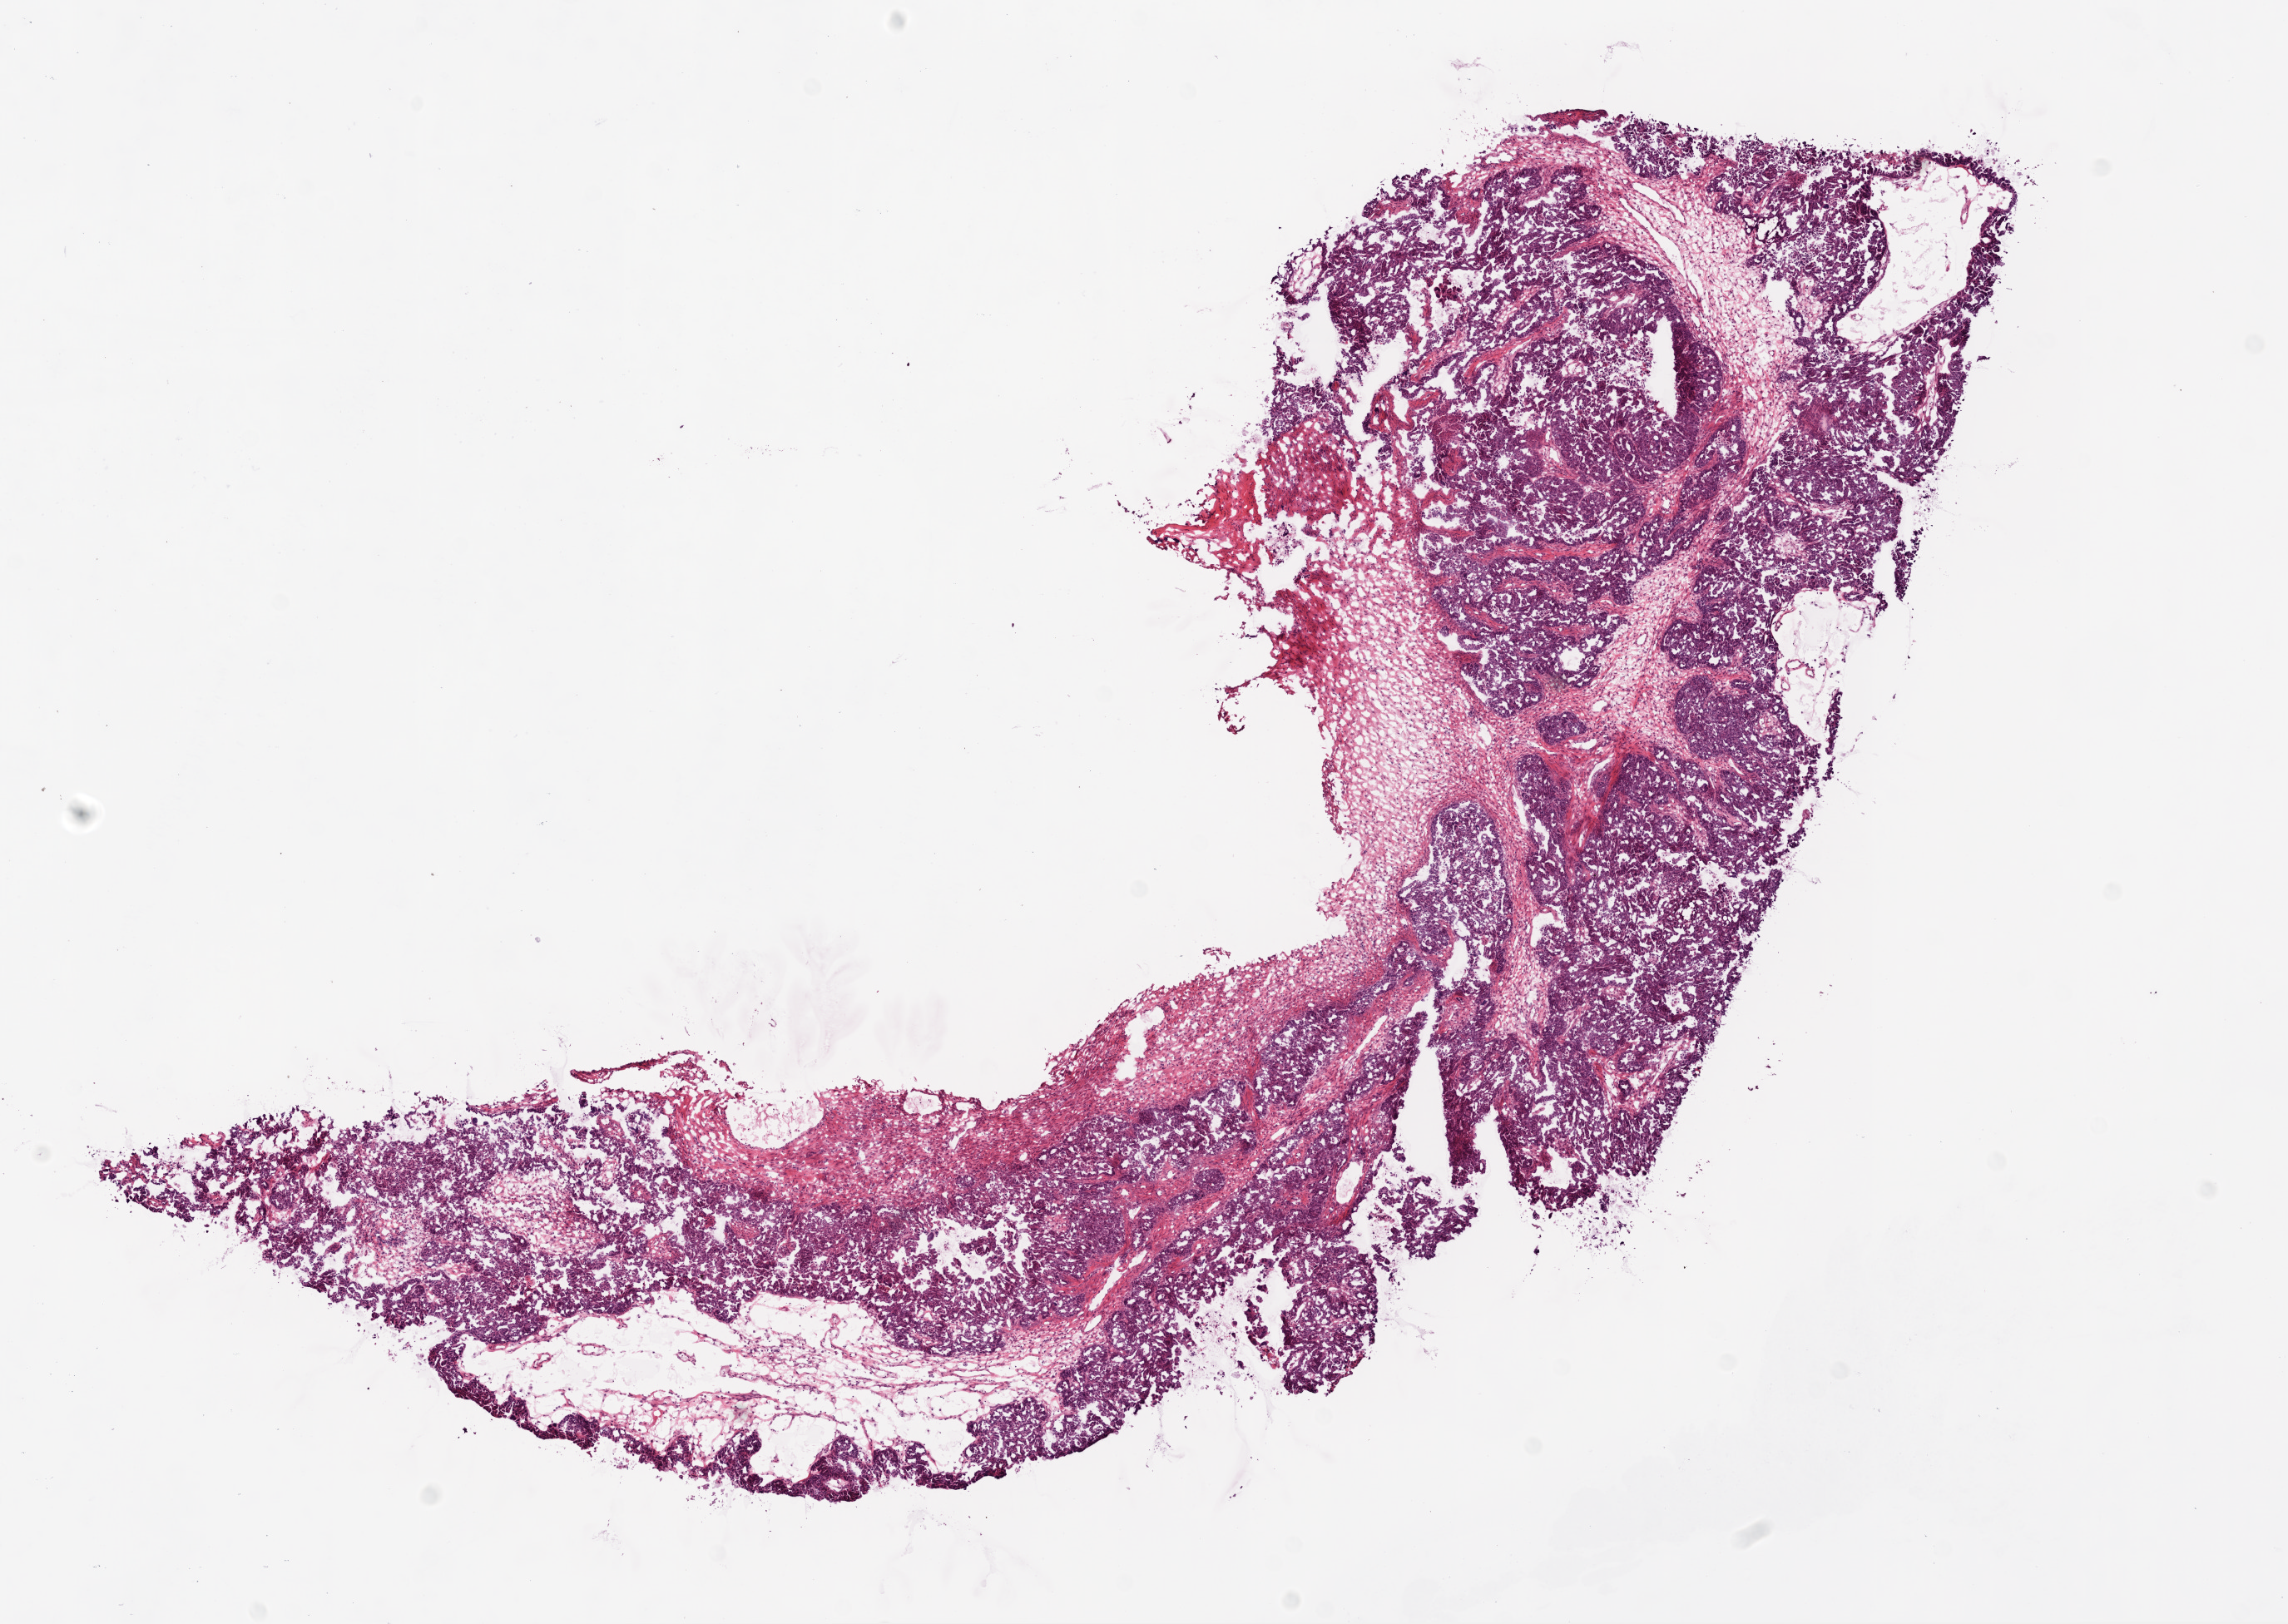
Whole-slide histology image, Hematoxylin and eosin (H&E) stained, whole scanned area (about 11.0 x 7.8 mm, from a 20x scan) shown as a low-resolution overview. Frozen section from the top of the tissue portion. Primary tumour sample from the ovary. Patient: female, age at initial diagnosis 54 years. Histologic grade: G3 (poorly differentiated). Pathologist review of this section (percent, as recorded): tumour cells 65%, tumour nuclei 80%, normal cells 0%, stromal cells 30%, necrosis 5%.
• histologic diagnosis: Serous cystadenocarcinoma, NOS
• laterality: right
• FIGO stage: IIIA